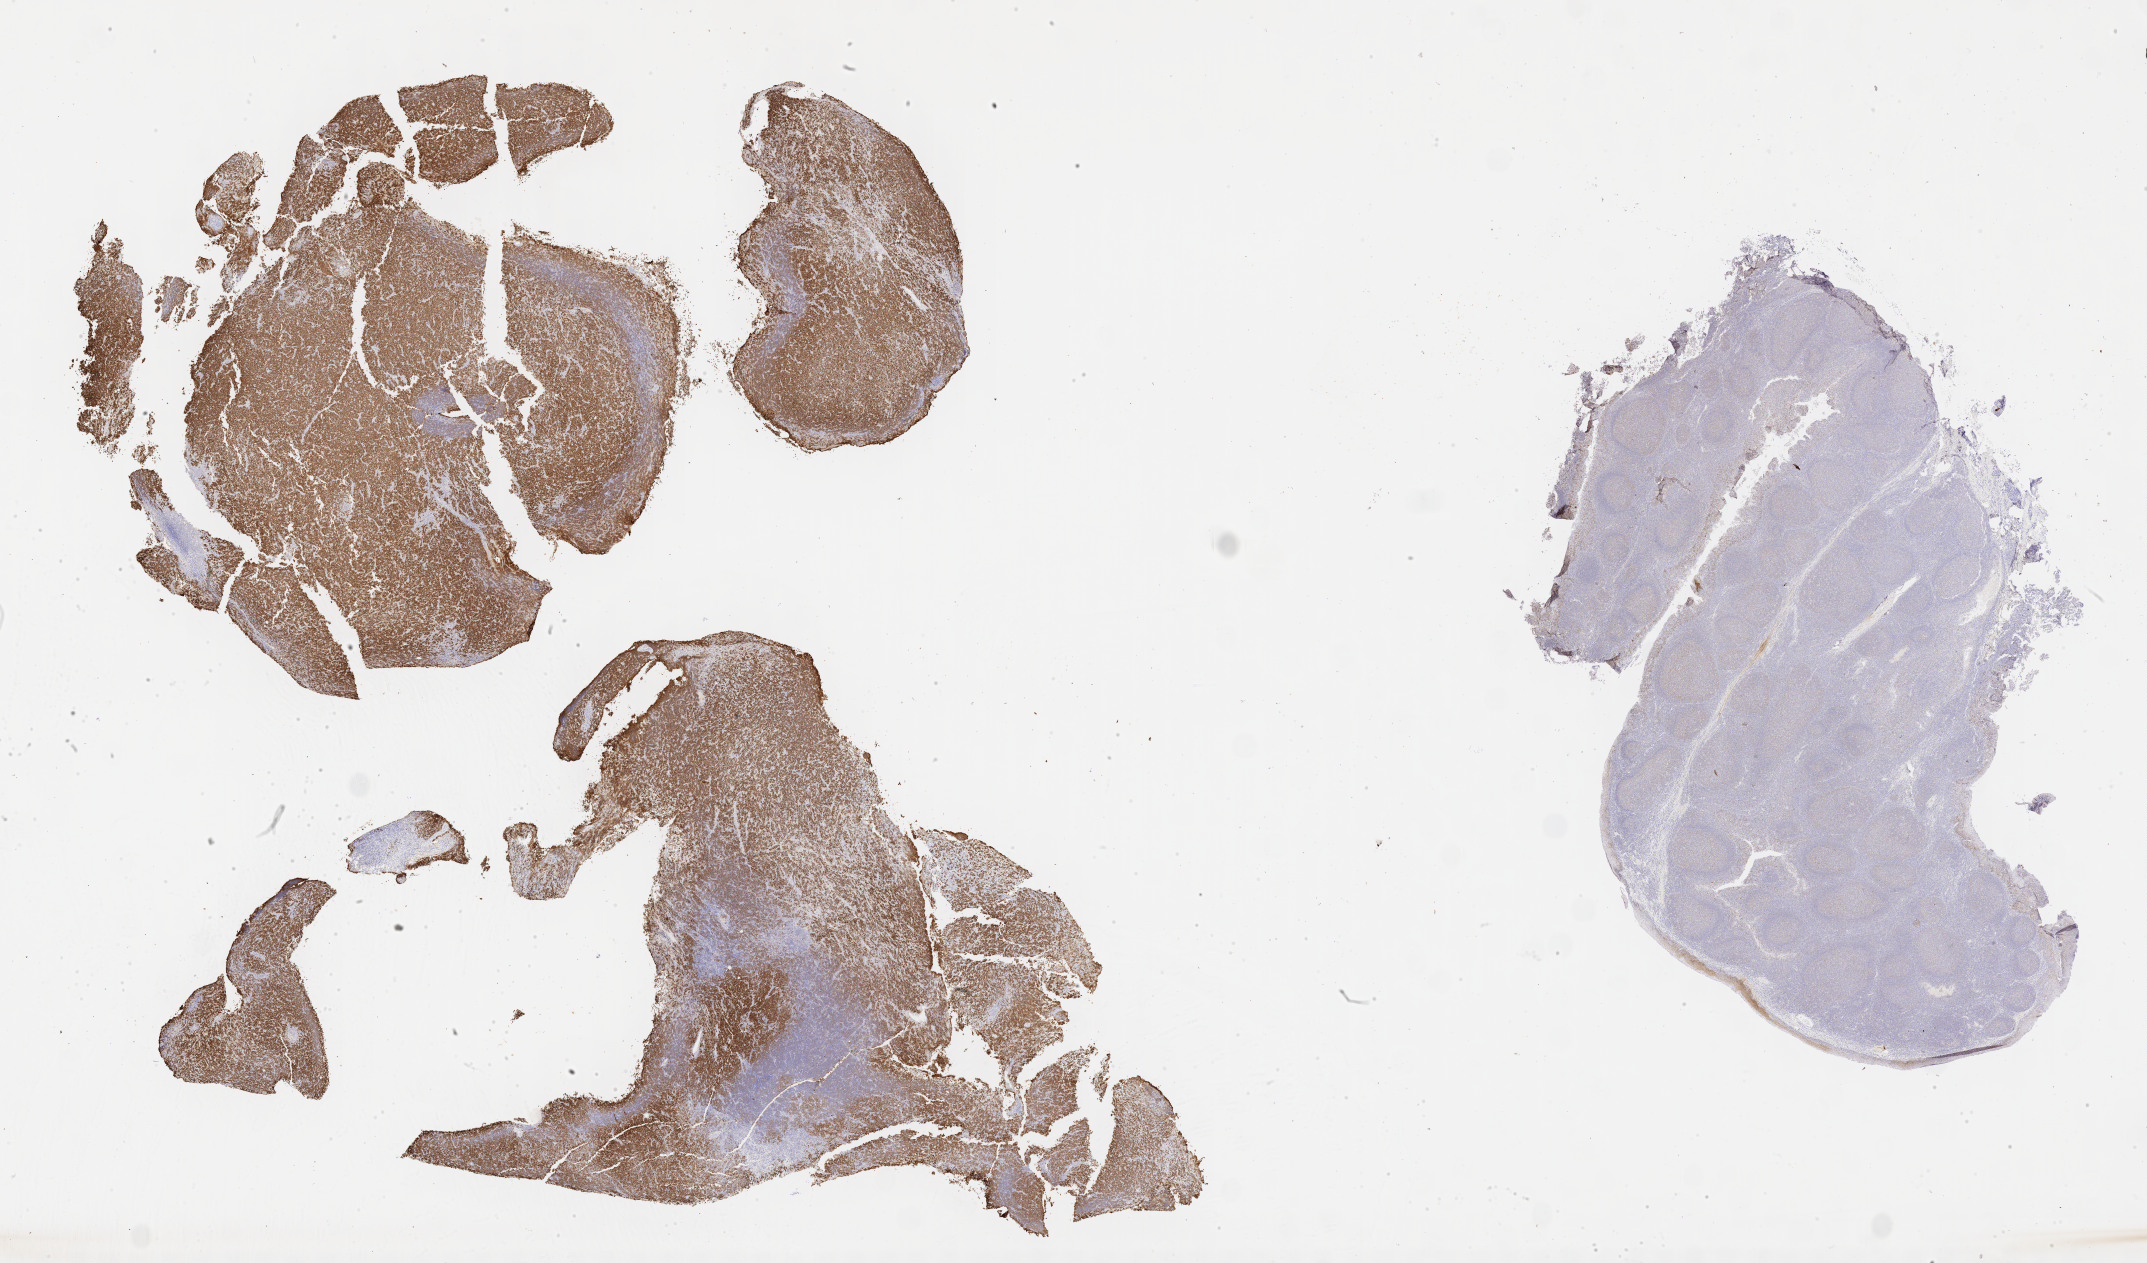
IHC for p53, whole-slide image, low-resolution overview of the scanned area, about 34.7 x 20.4 mm. Tumor tissue. Anatomic site: liver. Patient male; 45 years old.
• diagnosis: Diffuse large B-cell lymphoma, NOS